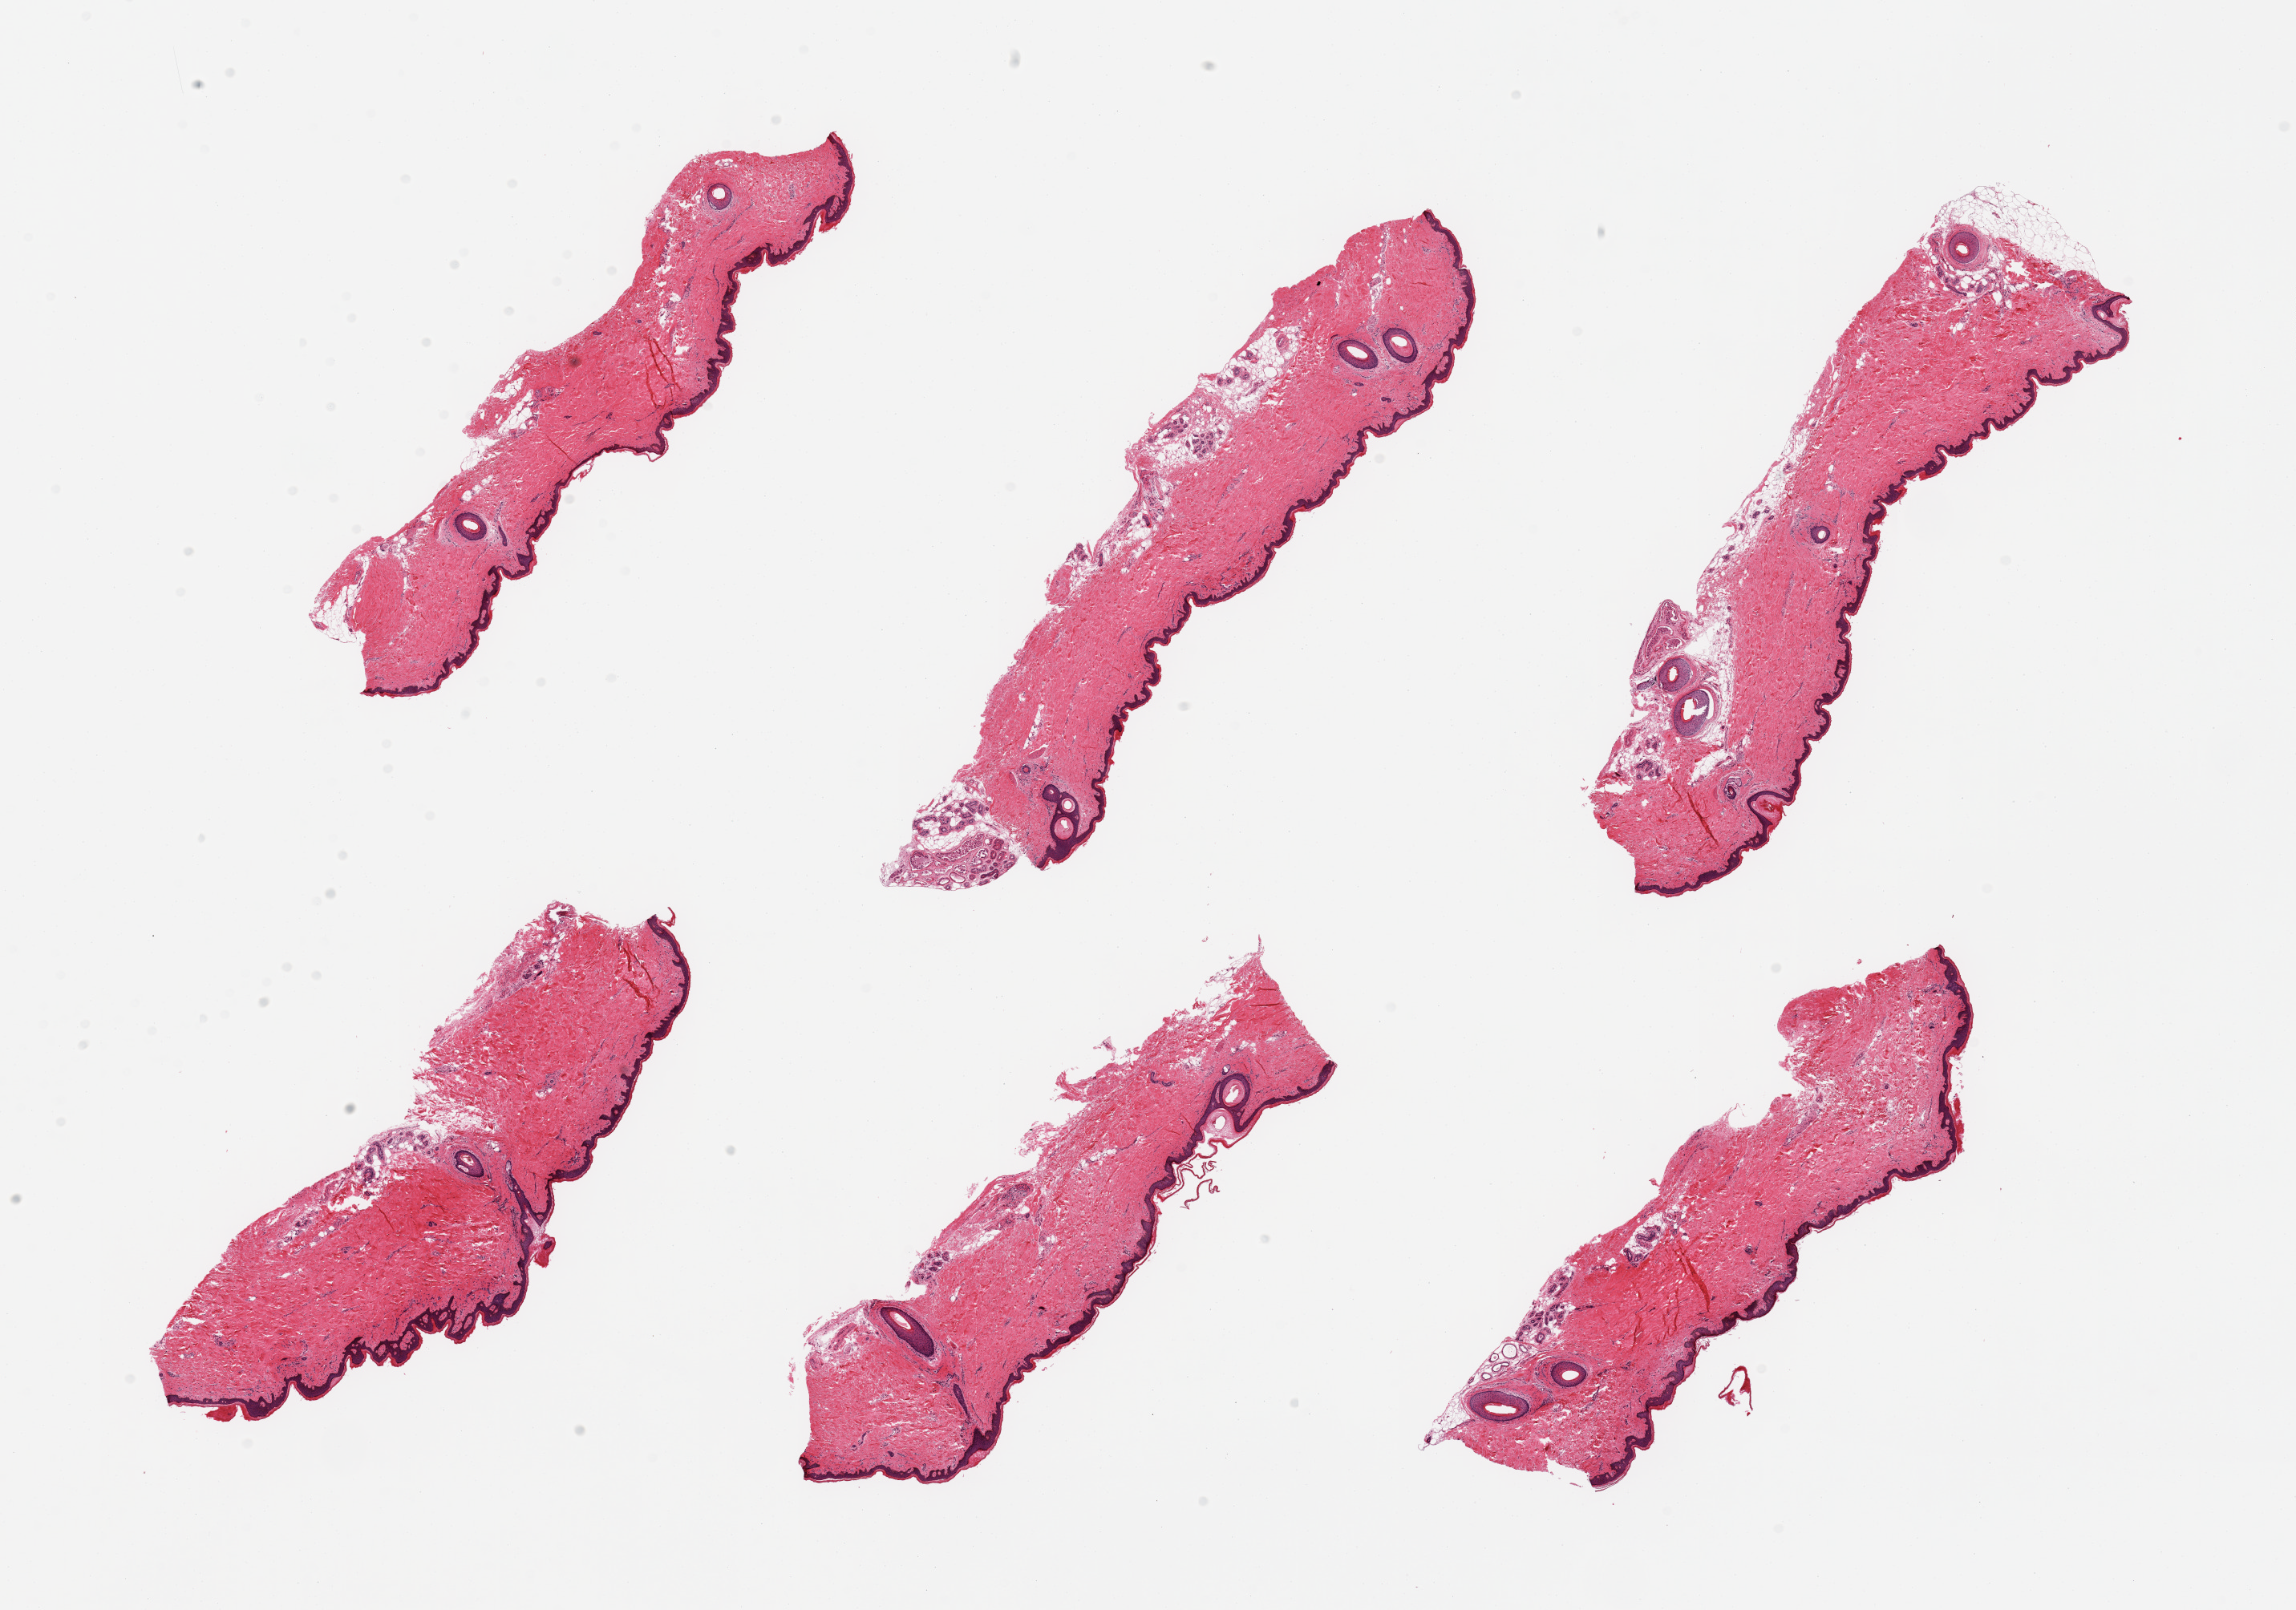
Hematoxylin and eosin (H&E) whole-slide image — low-resolution overview of the scanned area, about 22.6 x 15.9 mm (acquisition: 20x scan). PAXgene-fixed paraffin-embedded (PFPE) section. Sampled site (target tissue): skin of suprapubic region. Tissue donor sample.
Review note (as recorded): 6 pieces, minimal dermal fat; squamous epithelium is ~60 microns.